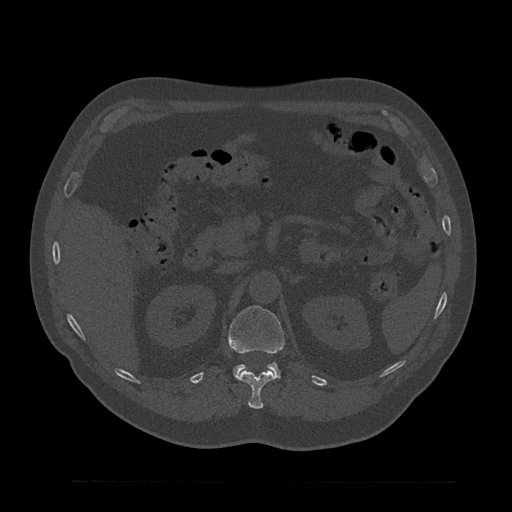
CT including the spine, one axial slice; reconstruction kernel Br40s/3; 120 kVp; bone window (W 1800 / L 400 HU); 0.5 mm slice thickness; 512 × 512 image matrix, field of view 430 × 430 mm. Patient: male, 61 years. Case-level facts recorded for this patient, not image findings: primary cancer: prostate.
Annotated regions visible in this slice (semi-automatic segmentation, software-assisted and operator-edited):
- L1 vertebra: box from (x=228, y=306) to (x=284, y=378) px
- T12 vertebra: (x=237, y=370)–(x=276, y=409)